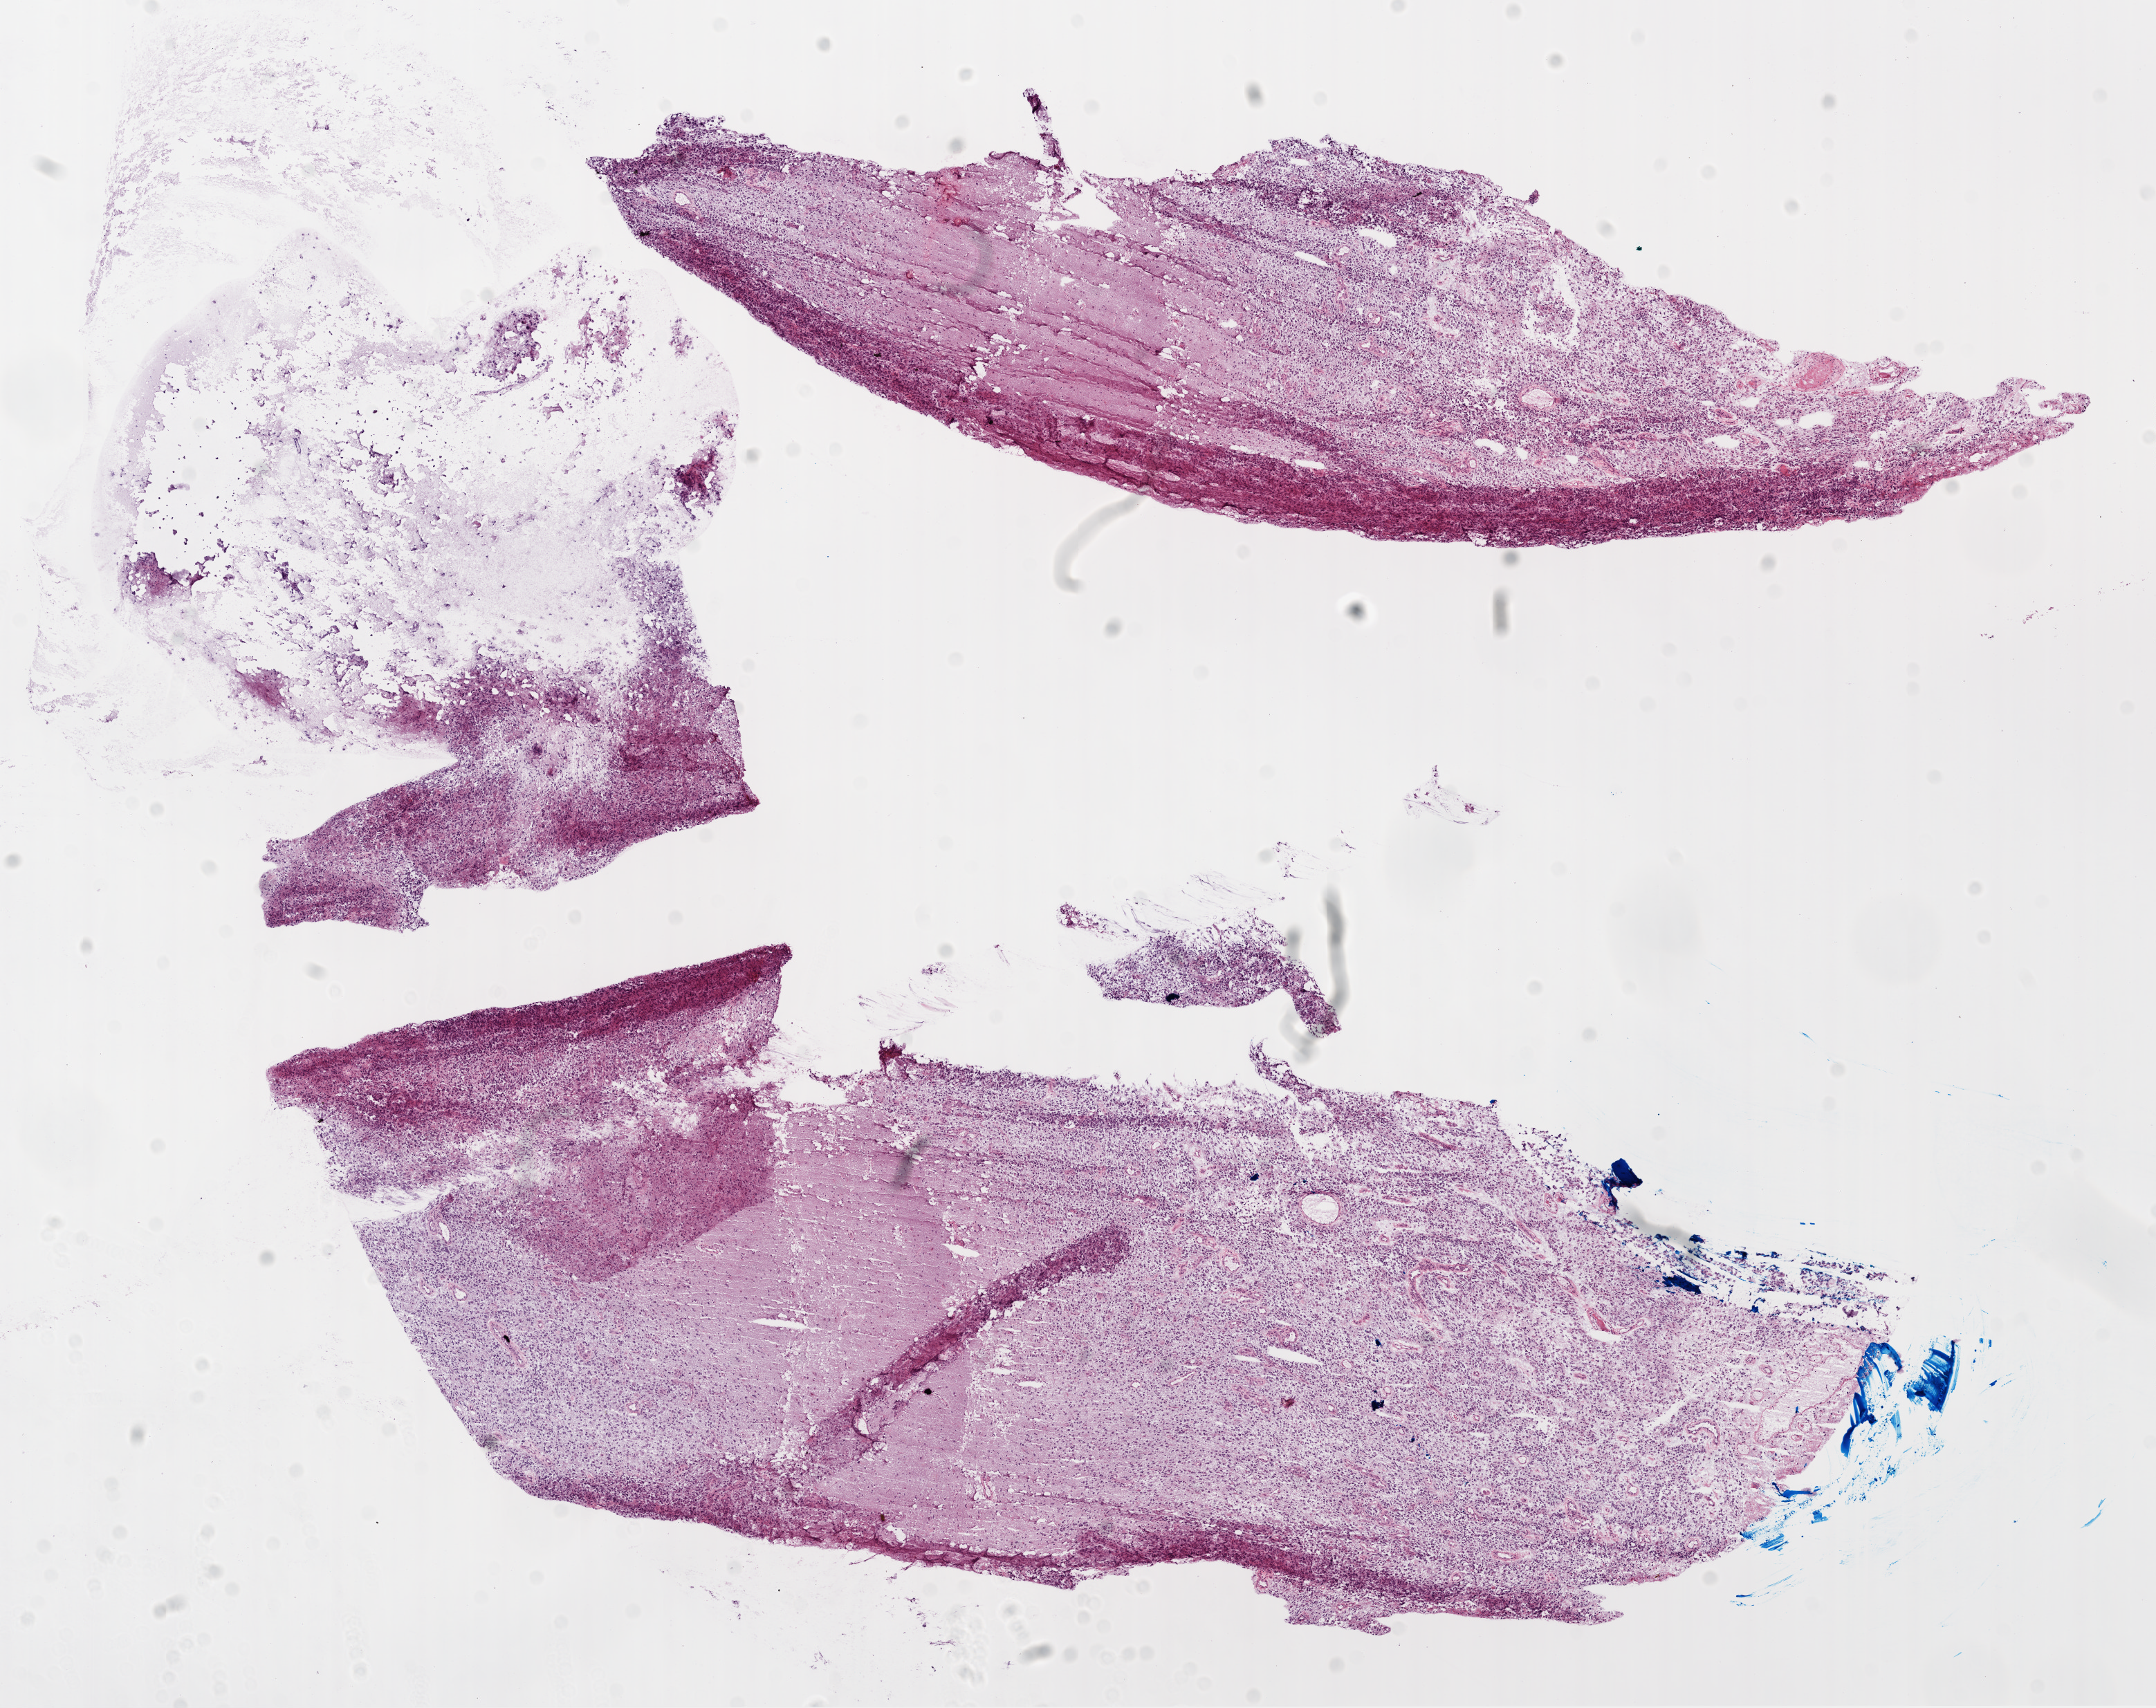
Whole-slide histology image, H&E-stained — a low-resolution overview of the entire scanned area, about 12.6 x 10.0 mm, frozen section from the top of the tissue portion, brain, primary tumour sample. Male, age 53 years at initial diagnosis. Composition of this section per pathologist review: tumour cells 75%, tumour nuclei 95%, normal cells 20%, stromal cells 0%, necrosis 5%.
• histologic diagnosis: Glioblastoma